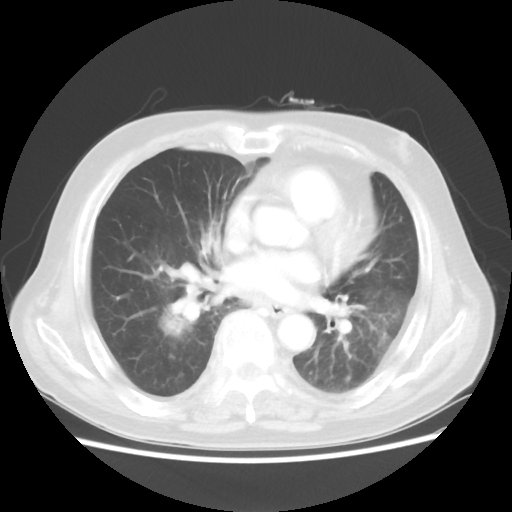
Chest CT, one axial slice; slice 18 of 44 in the series (ordered by position); reconstruction kernel STANDARD; 100 kVp; lung window (W 1500 / L -600 HU); 5 mm slice thickness; 512 × 512 image matrix. Male patient, age 83 years. From the clinical record (not read from this slice): clinical TNM (as recorded): T2 N3 M0.
Annotated regions visible in this slice (bounding box drawn by a radiologist):
- lung tumour (recorded histology: adenocarcinoma): bounding box [x1, y1, x2, y2] px = [157, 295, 204, 345]